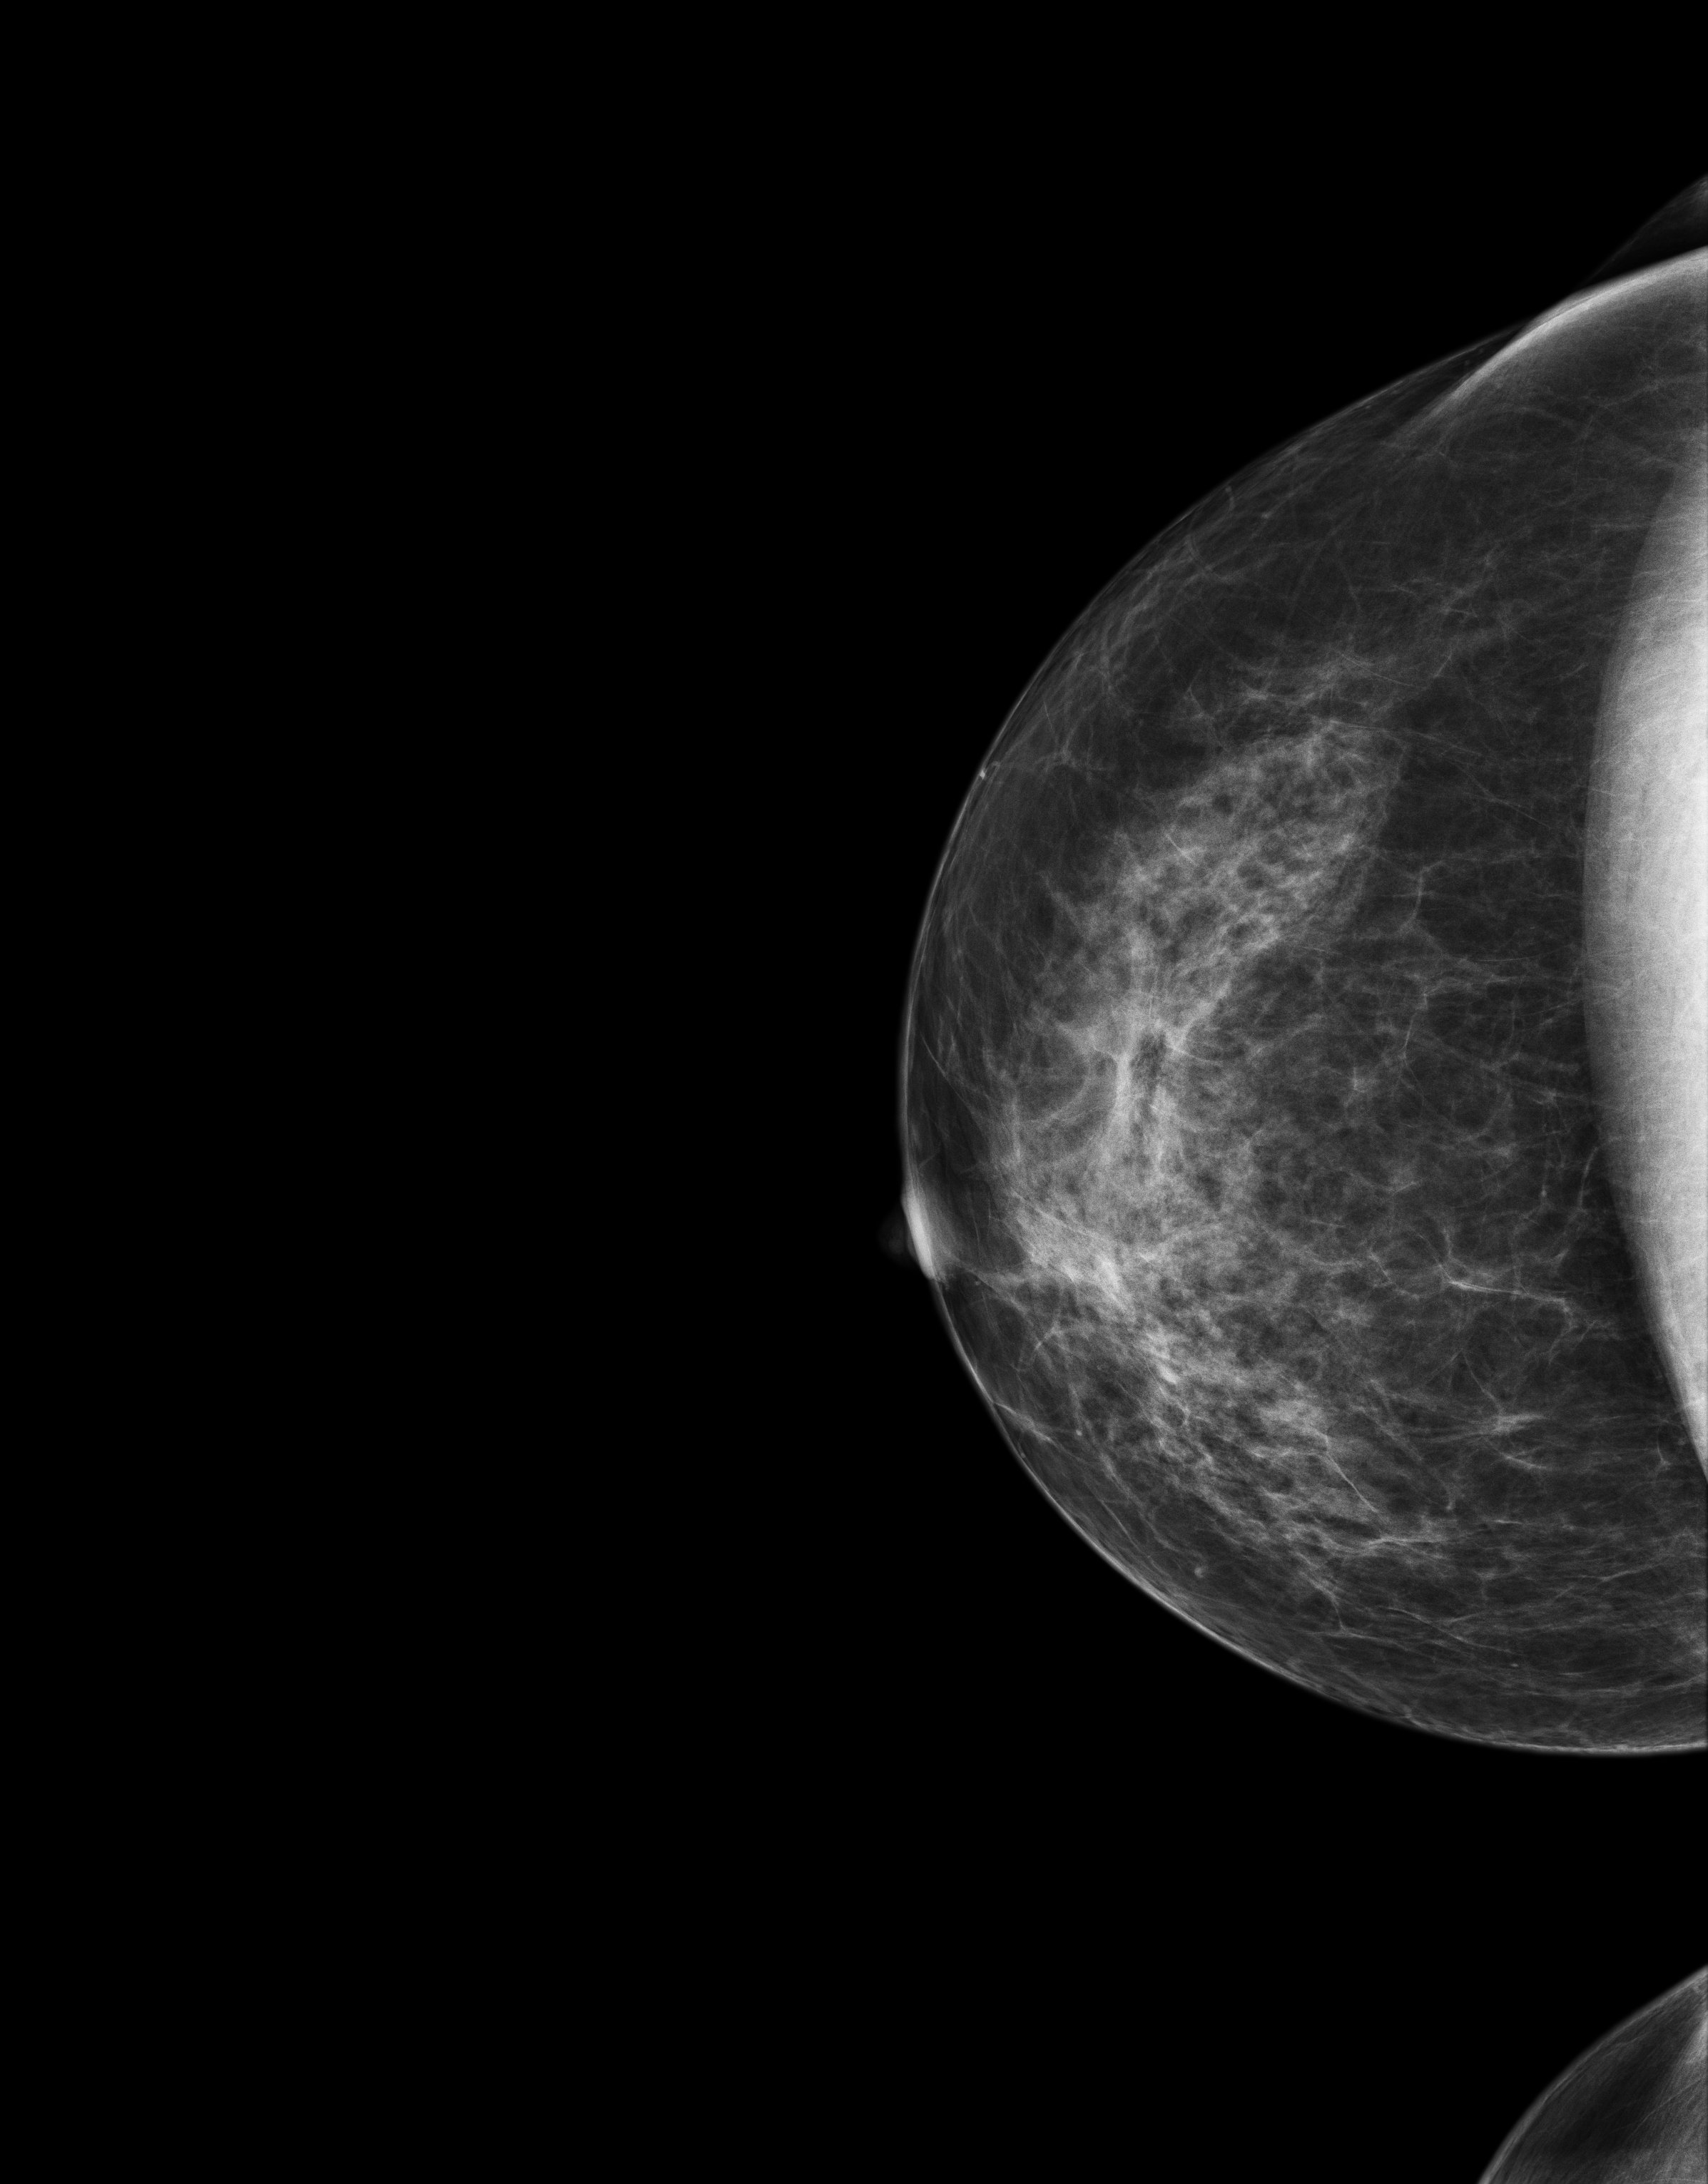
Screening examination, compressed breast thickness 58 mm. Female patient, age 54 years.
Image type: full-field digital mammogram. Breast: right. Projection: CC view.